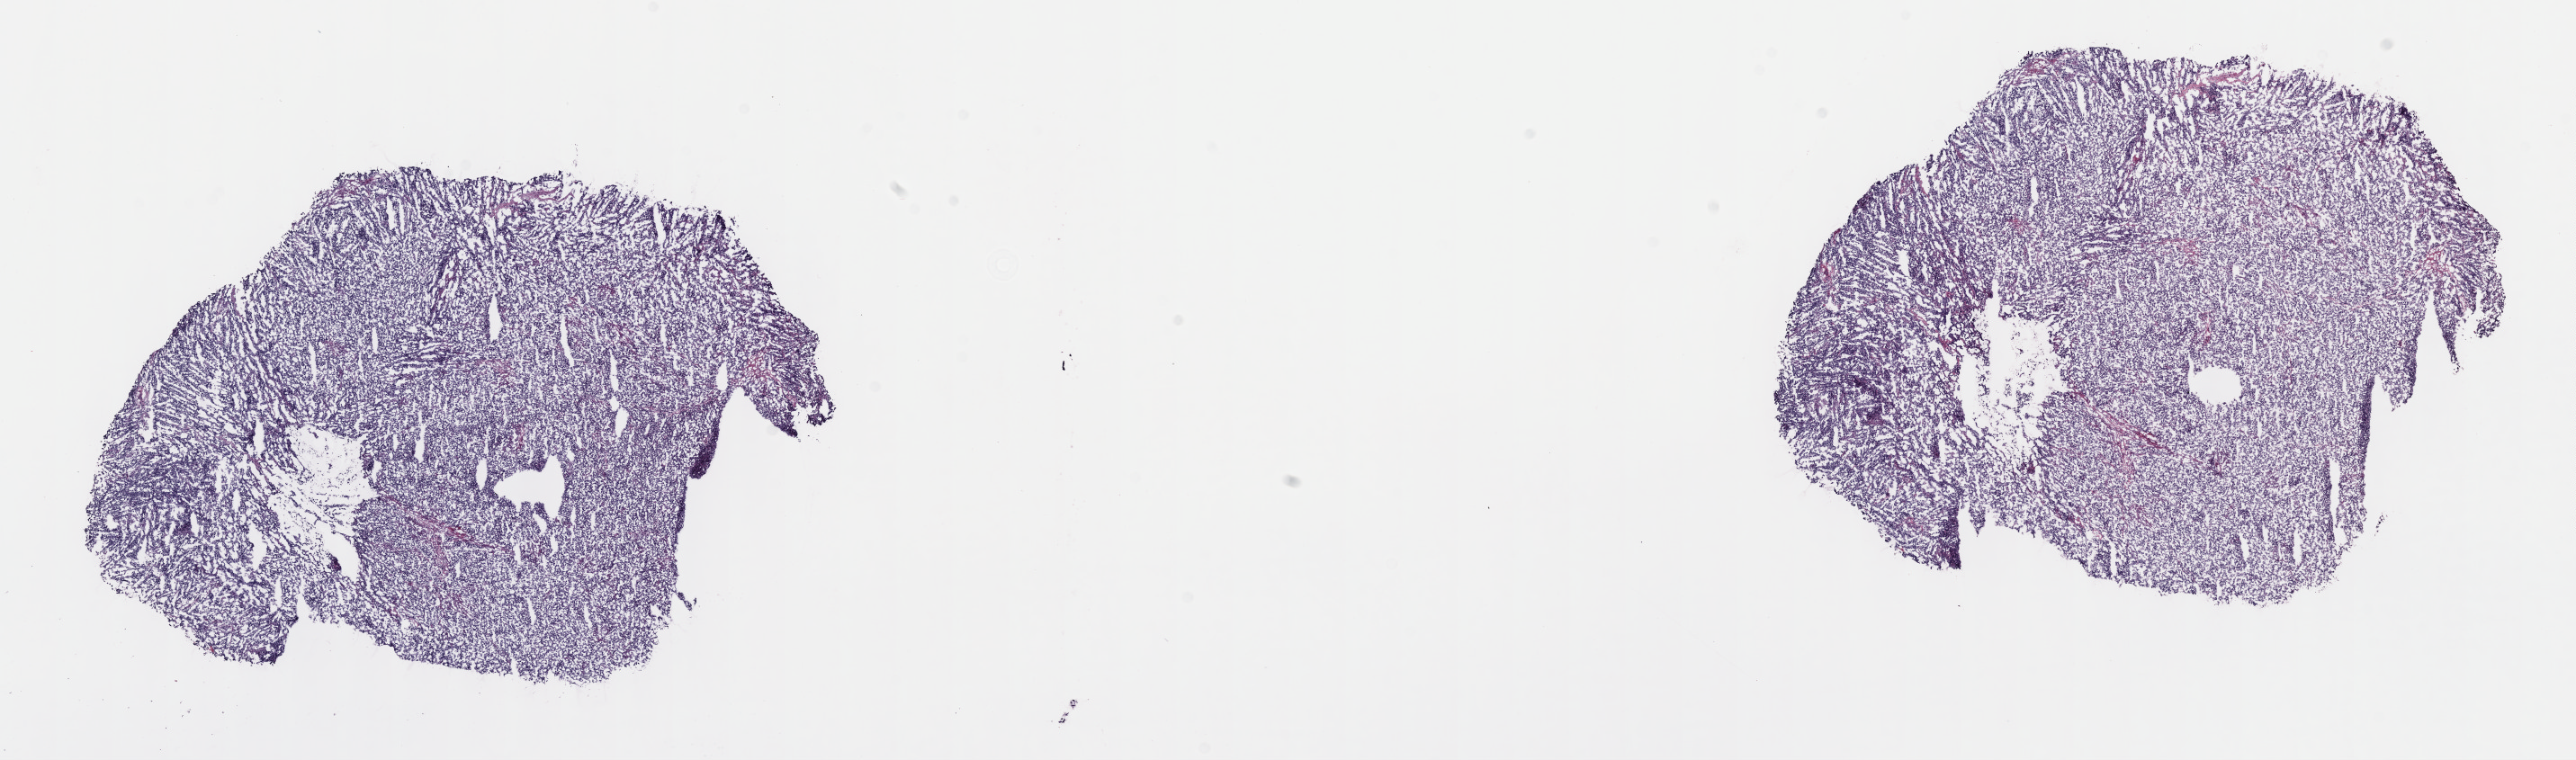
Digitized H&E tissue section (whole slide) — low-resolution overview of the scanned area, about 23.2 x 6.8 mm (acquisition: 40x scan); frozen section; testis, primary tumour sample. Patient: male, age at initial diagnosis 39 years. Composition of this section per pathologist review: tumour cells 80%, tumour nuclei 80%.
Diagnosis: Seminoma, NOS.